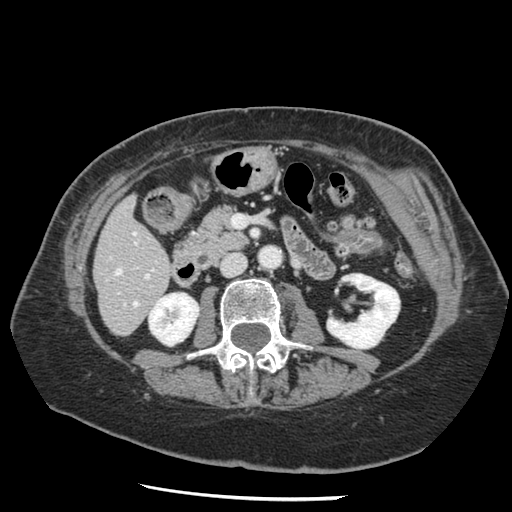
Contrast-enhanced abdominal CT, one axial slice; position 48 of 148 along the scan axis; reconstruction kernel STANDARD; 120 kVp; intravenous contrast given; soft-tissue window (W 400 / L 40 HU); 2.5 mm slice thickness; 512 × 512 image matrix. Female patient, age 85 years. From the clinical record (not read from this slice): diagnosis: colorectal cancer liver metastases, imaged before liver resection; multiple liver metastases: no; largest metastasis: 0.9 cm.
Annotated regions visible in this slice (manually delineated by an expert):
- hepatic veins: bounding box [x1, y1, x2, y2] px = [116, 269, 137, 306]
- liver: [95, 199, 172, 335]
- planned liver remnant (the part of the liver to remain after resection): [95, 199, 172, 334]